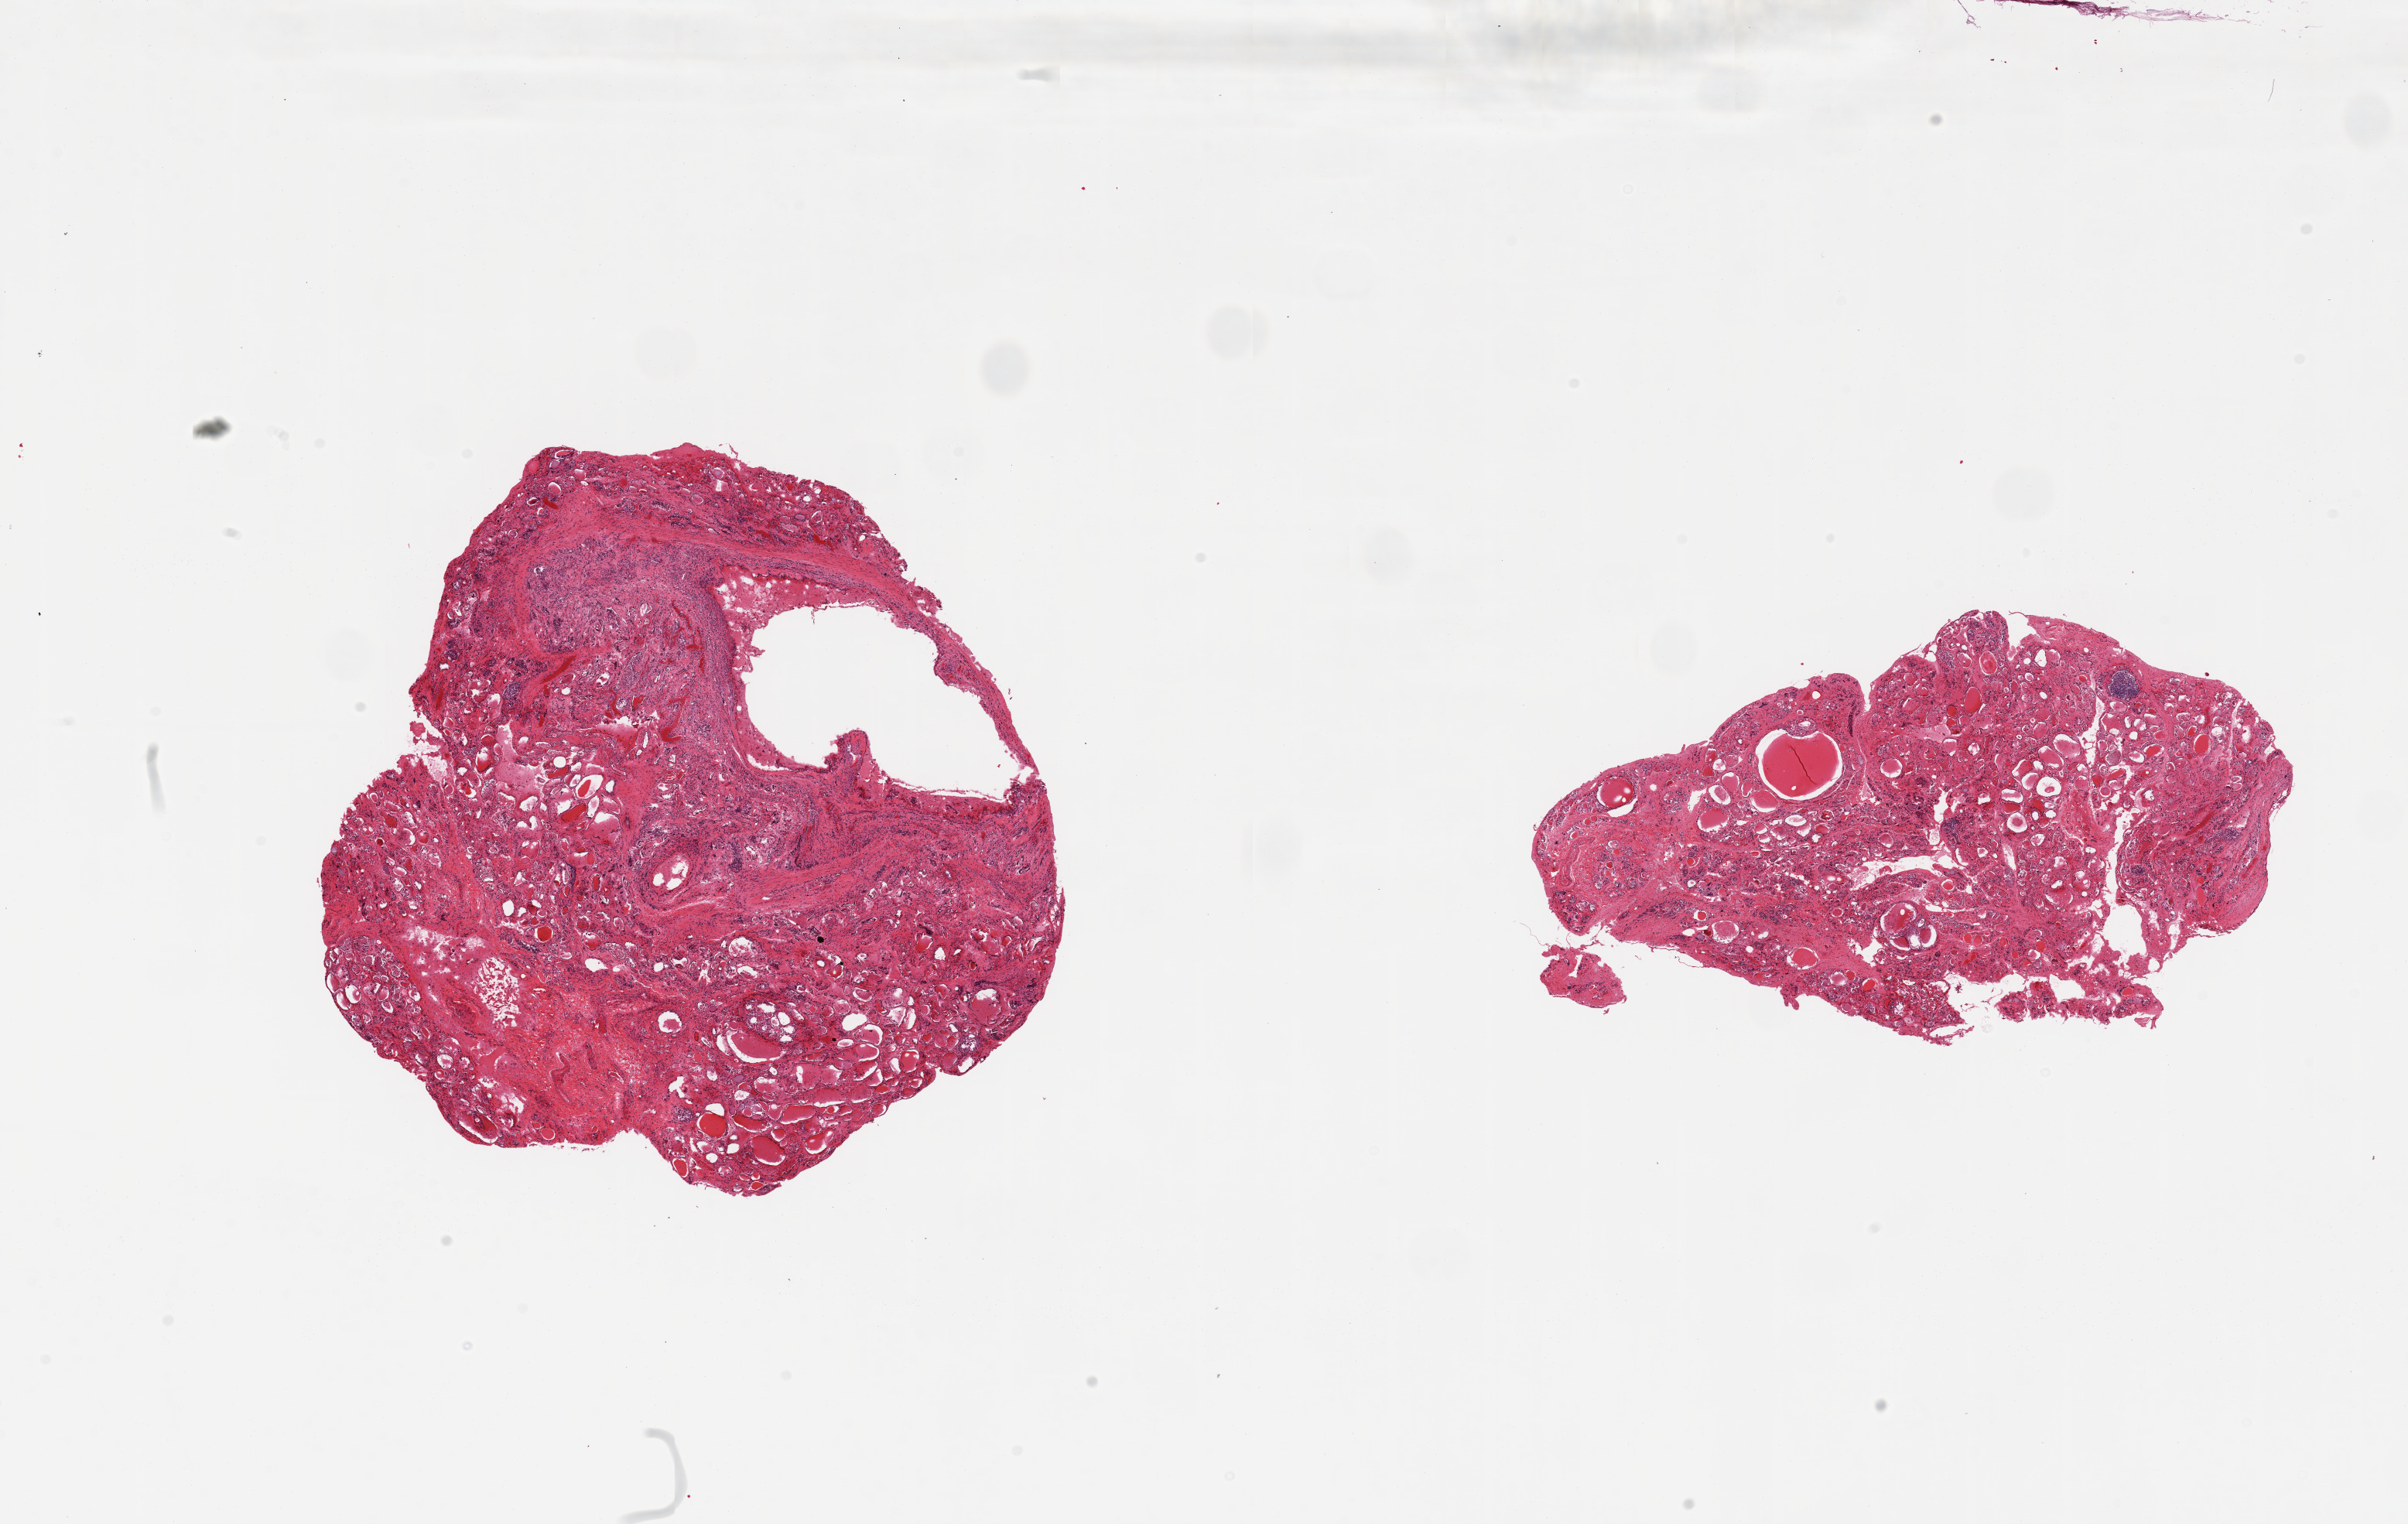
Whole-slide image, haematoxylin and eosin stain, brightfield — shown as a low-resolution overview of the whole scanned area (about 24.6 x 15.6 mm, slide scanned at 20x). PAXgene-fixed paraffin-embedded (PFPE) section. Sampled site (target tissue): thyroid. Tissue donor sample. Donor sex: female.
Reviewer comment on this tissue sample: 2 pieces; fibrosis and lymphoid infiltrate consistent with Hashimoto thyroiditis with nodular goiter.